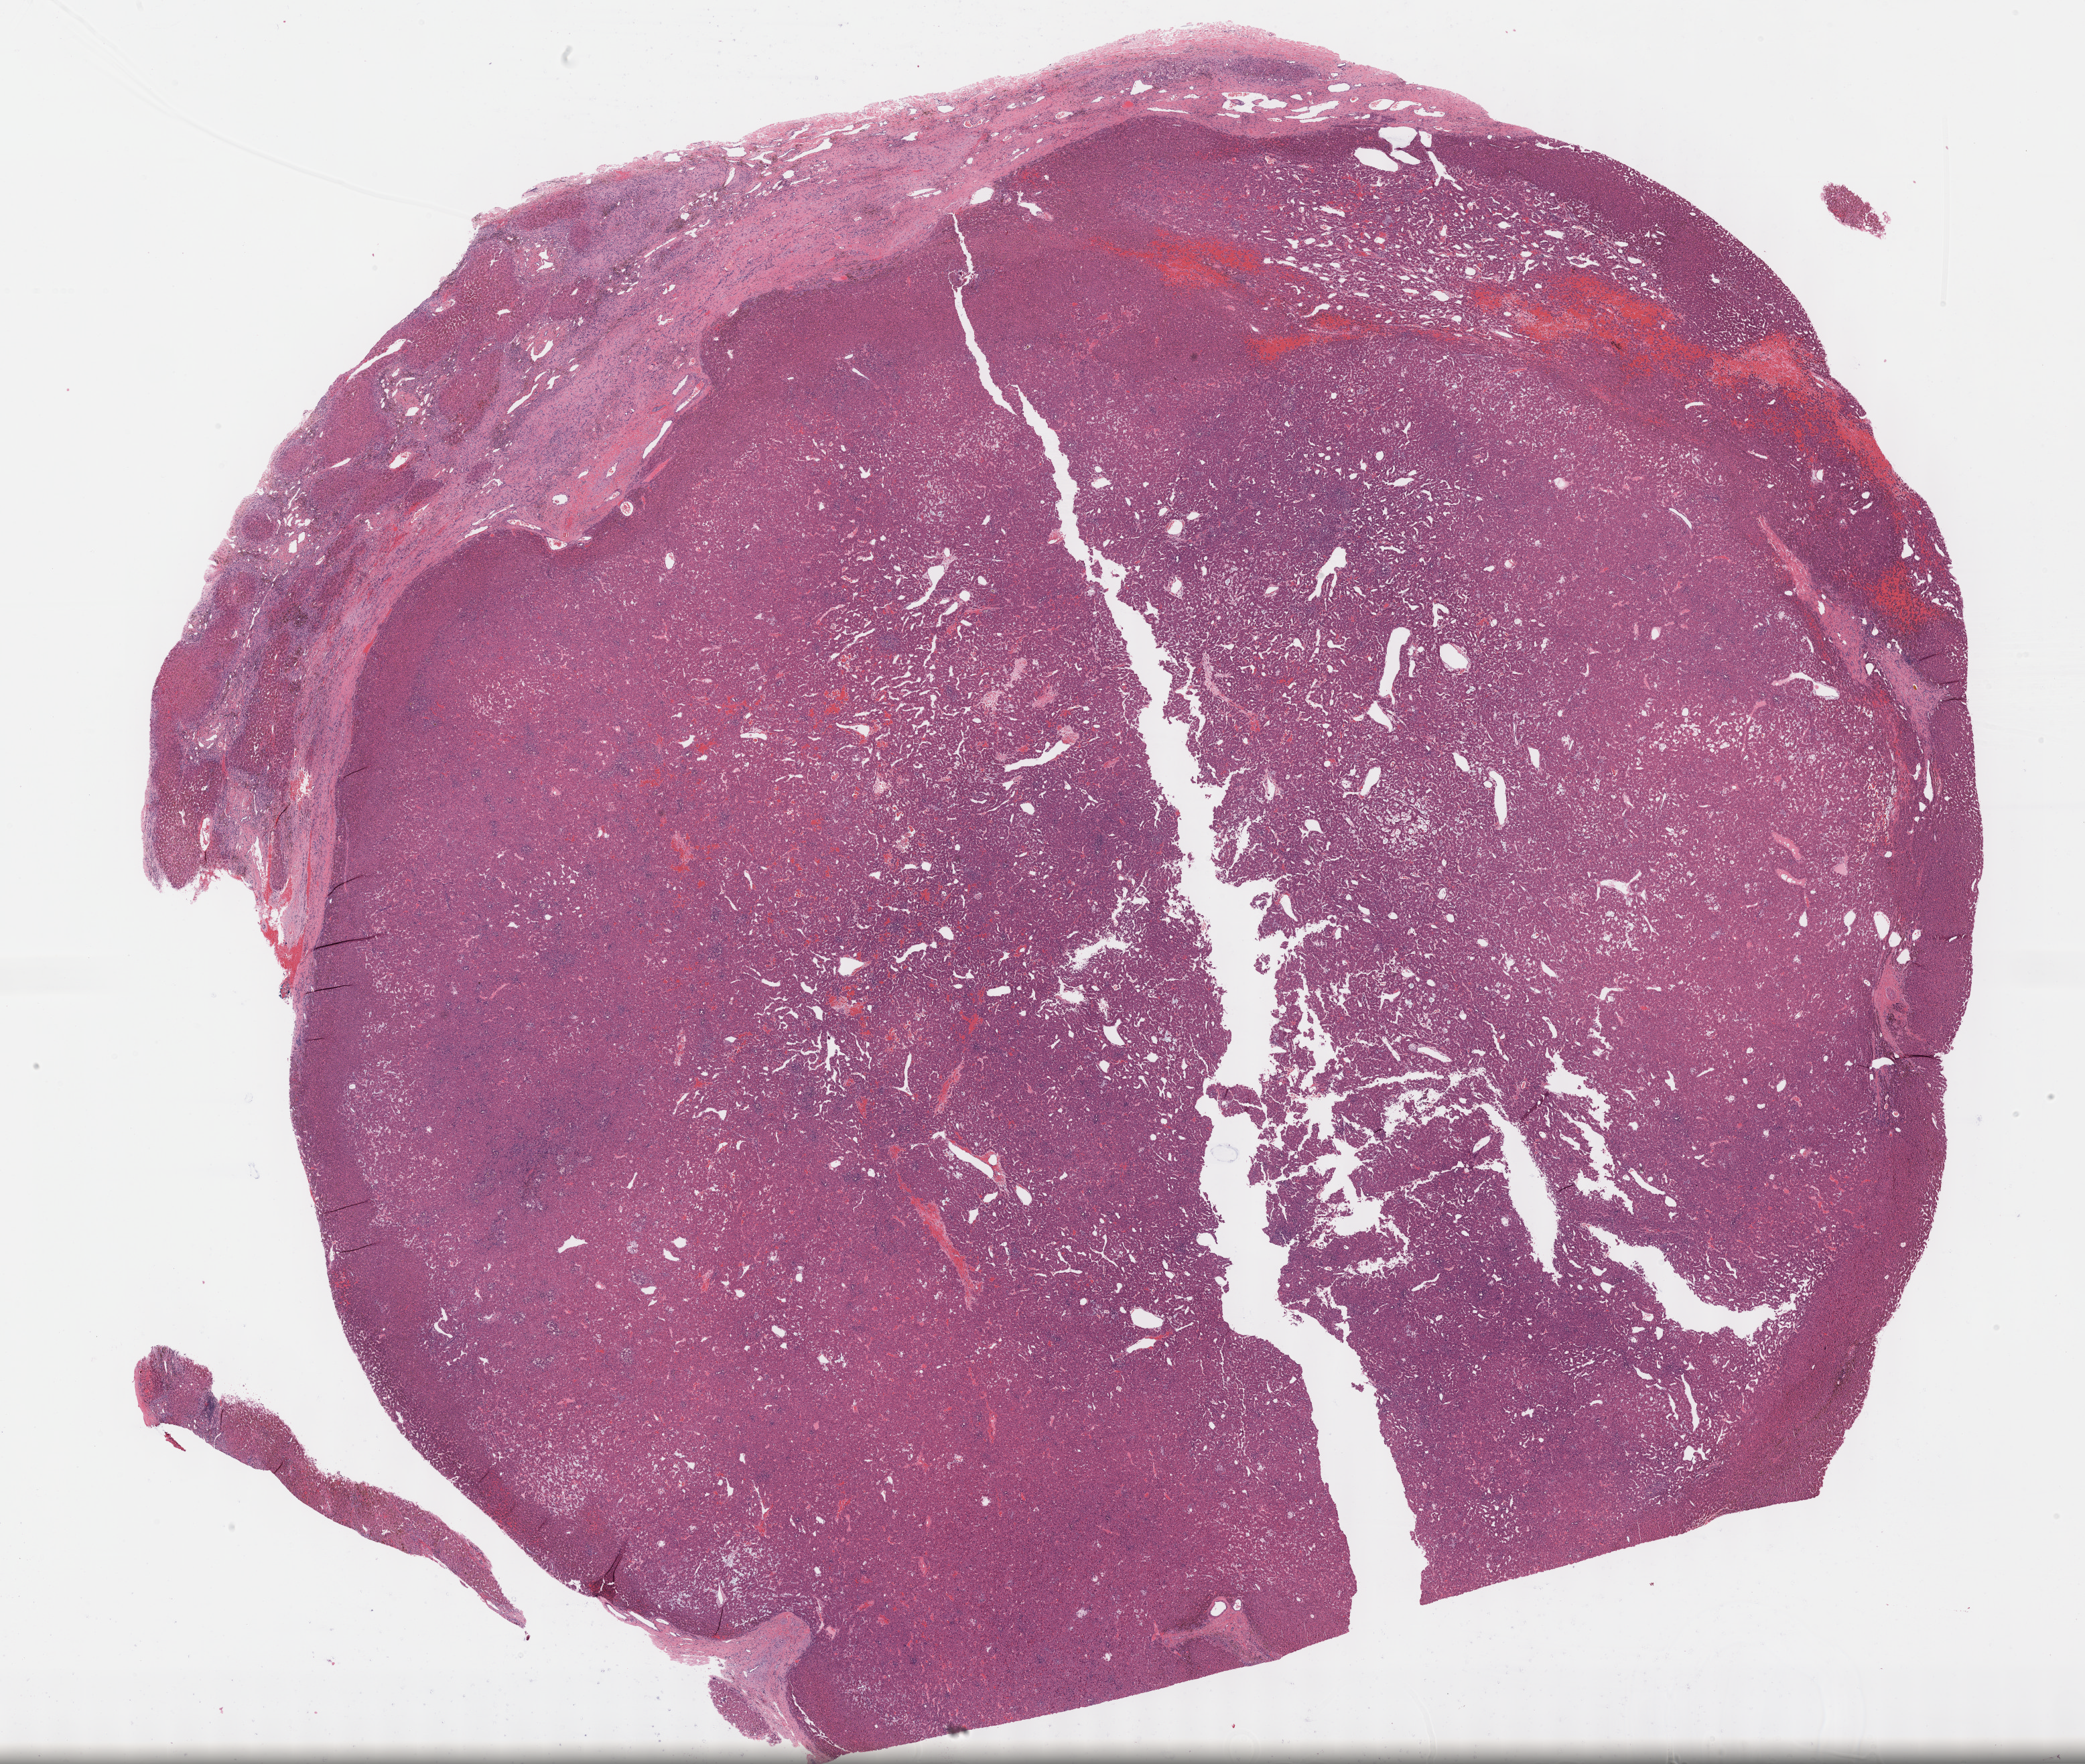
Whole-slide histology image, Hematoxylin and eosin (H&E) stained — shown as a low-resolution overview of the whole scanned area (about 25.2 x 21.3 mm, slide scanned at 40x); FFPE section; sample: primary tumour, liver. Male, age 31 years at initial diagnosis. Histologic grade: G1 (well differentiated).
TNM: T1 NX MX. Pathologic diagnosis: Hepatocellular carcinoma, NOS. AJCC pathologic stage: I (7th edition).